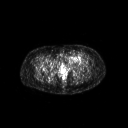
FDG PET of an extremity soft-tissue mass (from a PET/CT study), one axial slice. Slice 45 of 267 in the series (ordered by position). 128 × 128 image matrix, field of view 700 × 700 mm. Patient: female, 47 years. Case-level facts recorded for this patient, not image findings: histological type: myxofibrosarcoma; grade: intermediate; site of the primary tumour: left thigh.
Annotated regions visible in this slice (expert contour drawn on MRI and transferred to this co-registered scan by the dataset authors):
- gross tumour volume including surrounding oedema: box from (x=65, y=54) to (x=84, y=63) px
- gross tumour volume (mass): (x=71, y=54)–(x=77, y=60)